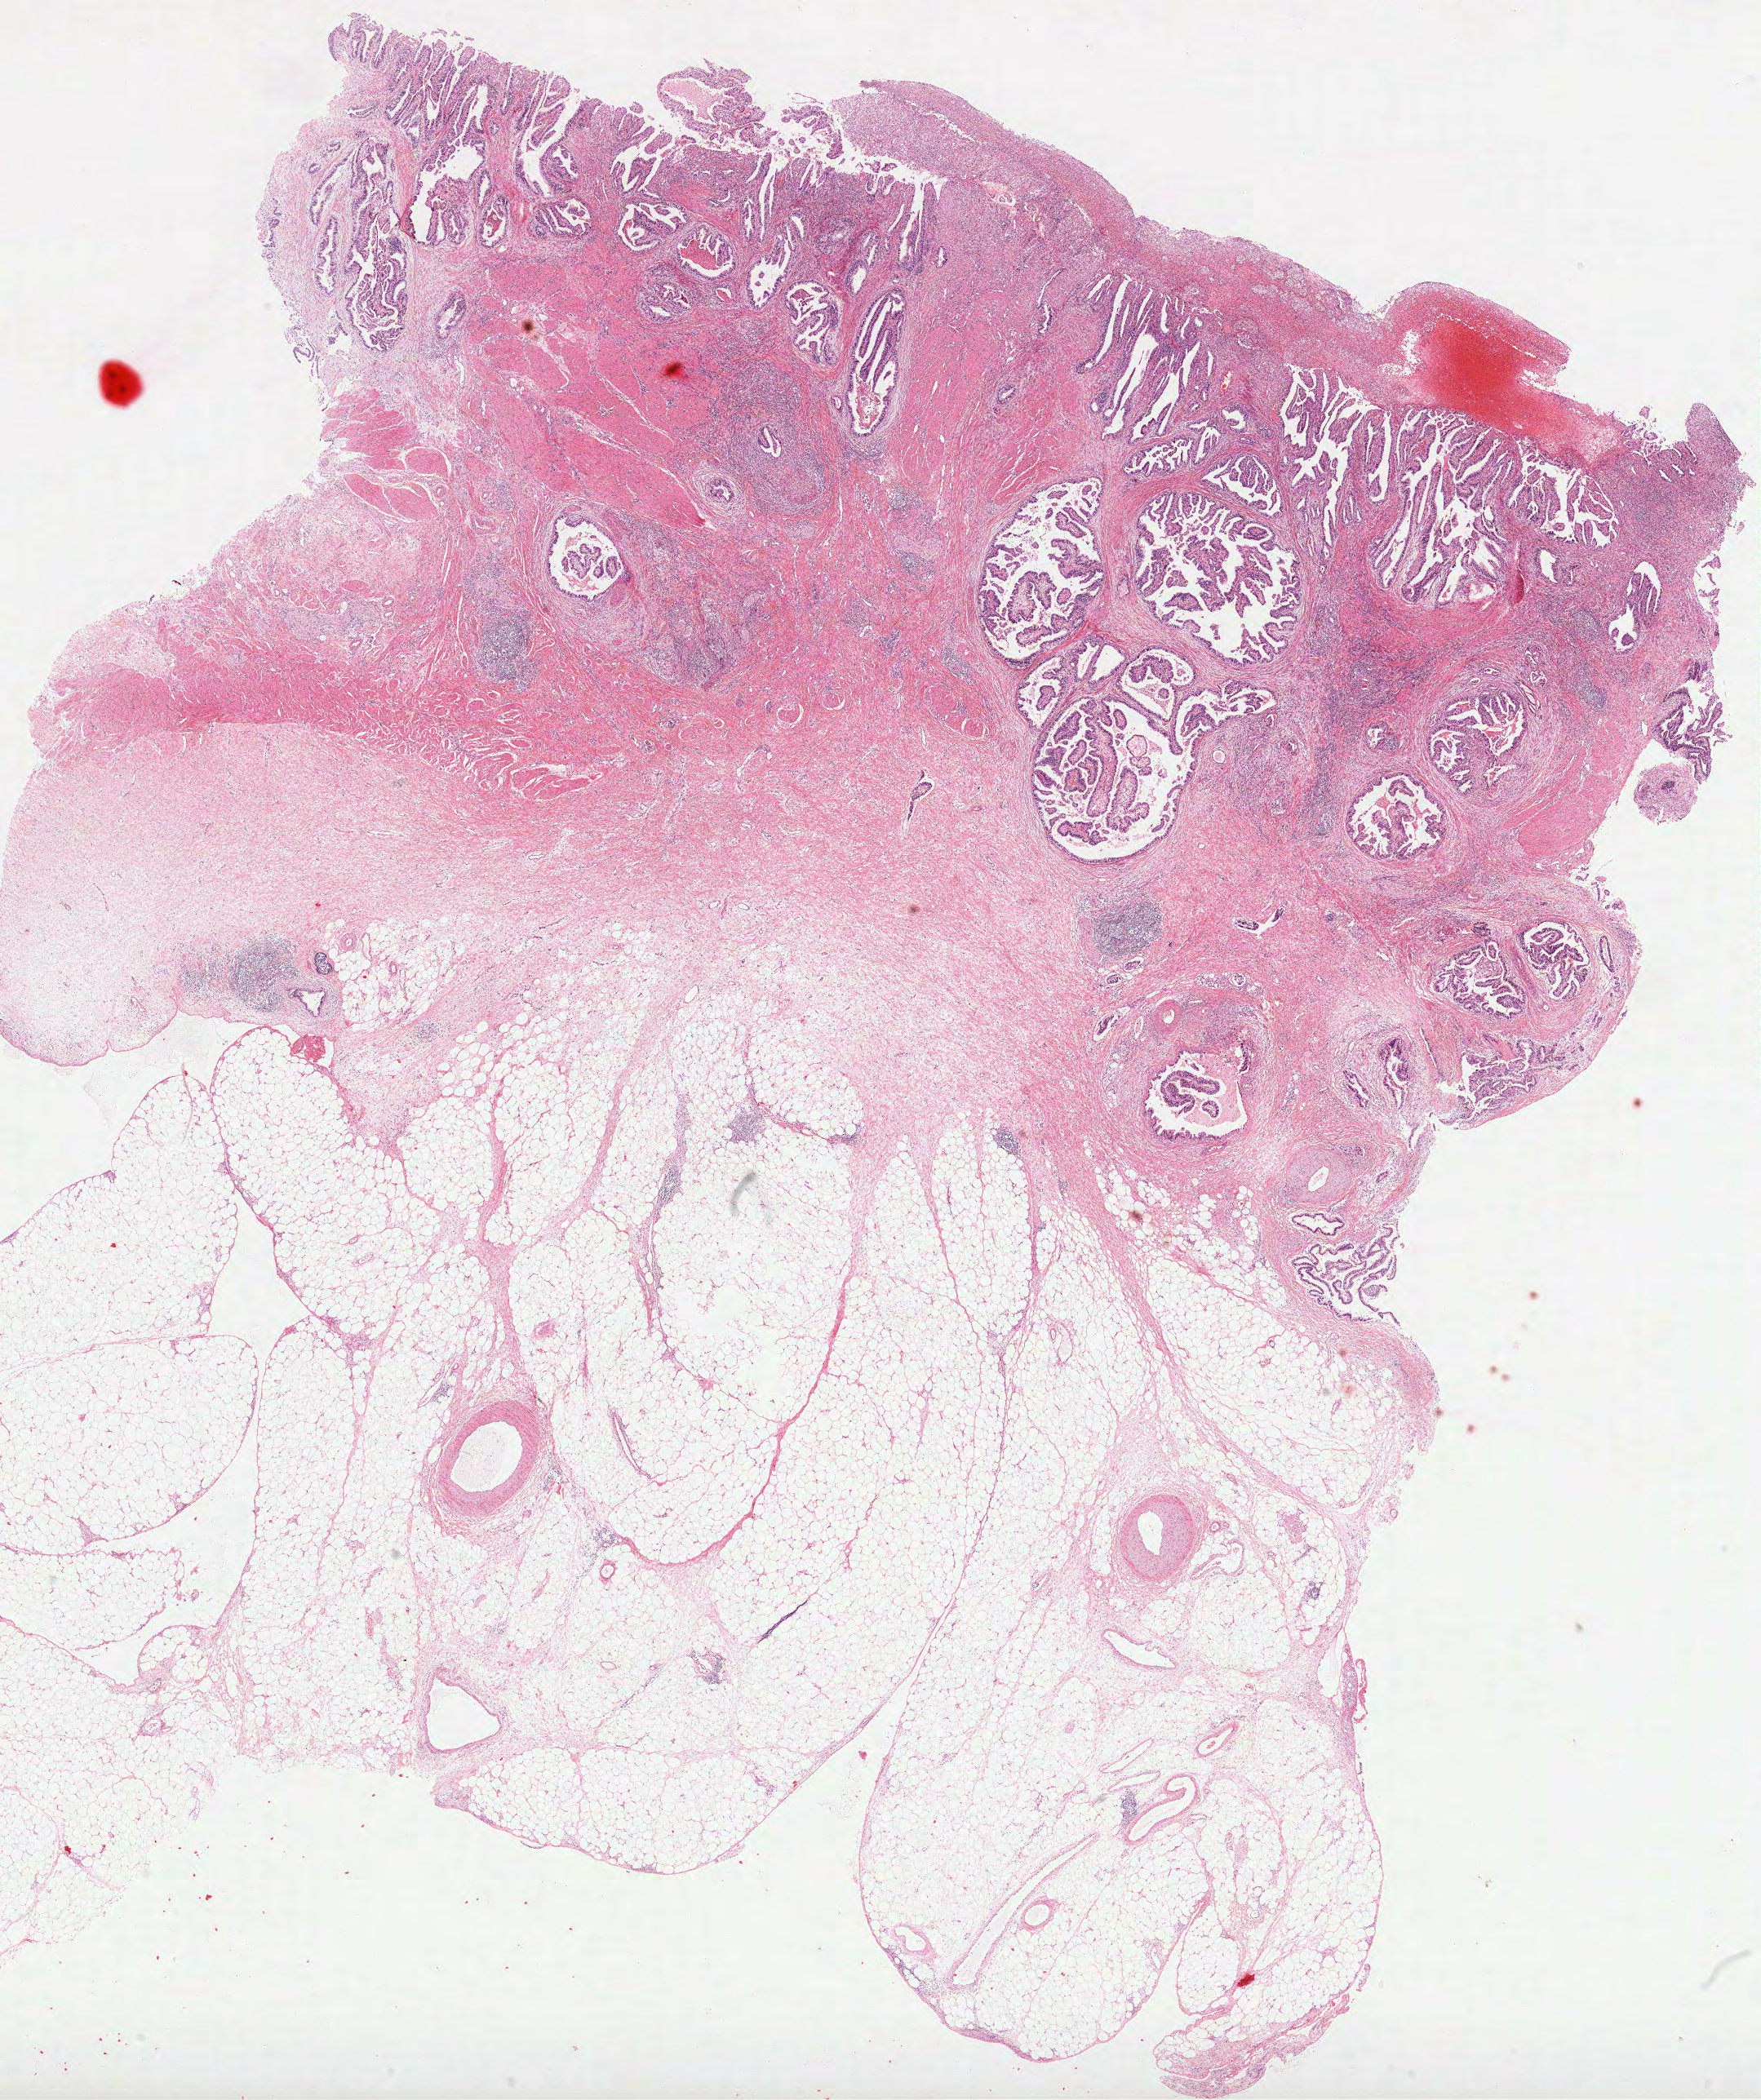
H&E whole-slide image, shown as a low-resolution overview of the whole scanned area (about 17.4 x 20.8 mm, from a 40x scan); formalin-fixed paraffin-embedded (FFPE) diagnostic section; stomach, primary tumour sample. Female patient; age at initial diagnosis 65 years. Histologic grade: G2 (moderately differentiated).
• lymph nodes positive (case pathology): 2 of 15 examined
• AJCC pathologic stage: IIIA (7th edition)
• diagnosis: Adenocarcinoma, intestinal type (fundus of stomach)